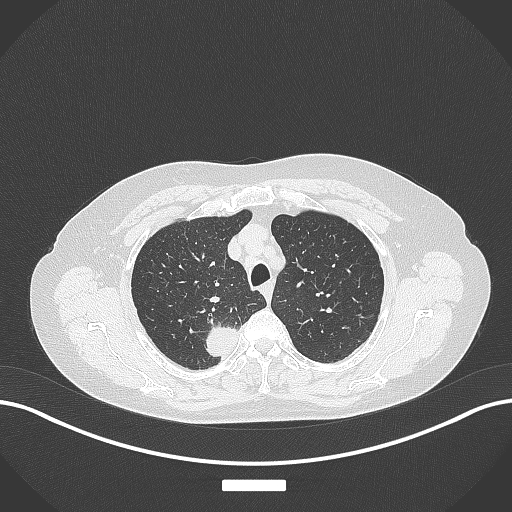
Chest CT, one axial slice. Slice 312 of 357 in the series (ordered by position). Reconstruction kernel B70f. 120 kVp. Lung window (W 1500 / L -600 HU). 1 mm slice thickness. 512 × 512 image matrix. Patient: female, 62 years. Case-level facts recorded for this patient, not image findings: clinical TNM (as recorded): T1c N1 M0.
Structures marked on this image (rectangle marked by the reading radiologist):
- lung tumour (recorded histology: squamous cell carcinoma): bounding box [x1, y1, x2, y2] px = [204, 315, 236, 364]